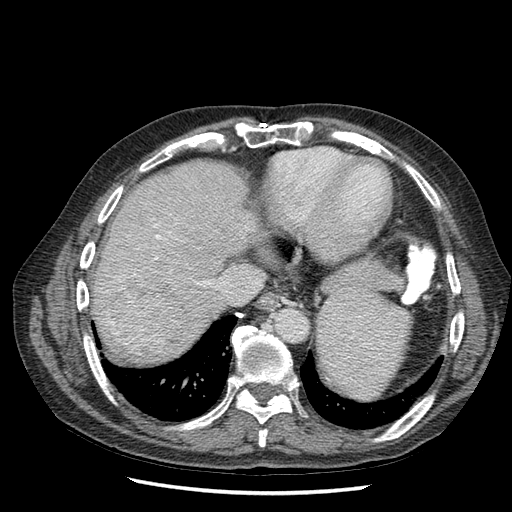
Contrast-enhanced abdominal CT (liver protocol), one axial slice. Position 57 of 67 along the scan axis. Reconstruction kernel STANDARD. Soft-tissue window (W 400 / L 40 HU). 2.5 mm slice thickness. 512 × 512 image matrix, field of view 360 × 360 mm. Case-level facts recorded for this patient, not image findings: diagnosis: hepatocellular carcinoma (patient treated with transarterial chemoembolisation; whether this scan precedes or follows treatment is not stated here); TNM stage (as recorded): Stage-I; Child-Pugh class: A; tumour differentiation: moderately differentiated; tumour nodularity: uninodular.
Outlined on this slice (semi-automatically segmented with operator editing):
- abdominal aorta: bounding box [x1, y1, x2, y2] px = [275, 307, 309, 340]
- liver parenchyma outside the tumour (the mass and vessels are separate outlines, so this box may not span the whole liver): [92, 158, 246, 356]
- mass: [102, 278, 183, 351]
- liver vessels: [132, 237, 172, 278]